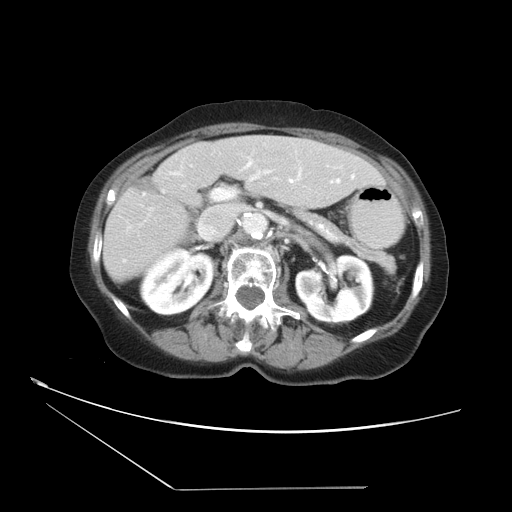
Contrast-enhanced abdominal CT, one axial slice. Slice 17 of 36 in the series (ordered by position). Intravenous contrast given. Soft-tissue window (W 400 / L 40 HU). 5 mm slice thickness. 512 × 512 image matrix, field of view 384 × 384 mm. Female patient, age 81 years. Case-level facts recorded for this patient, not image findings: diagnosis: colorectal cancer liver metastases, imaged before liver resection; multiple liver metastases: no.
Structures marked on this image (outlined manually by an expert reader):
- hepatic veins: bounding box (x1, y1, x2, y2) in pixels: (248, 162, 339, 183)
- liver: (104, 136, 385, 280)
- planned liver remnant (the part of the liver to remain after resection): (104, 140, 385, 281)
- portal vein (with intrahepatic branches): (215, 176, 257, 199)